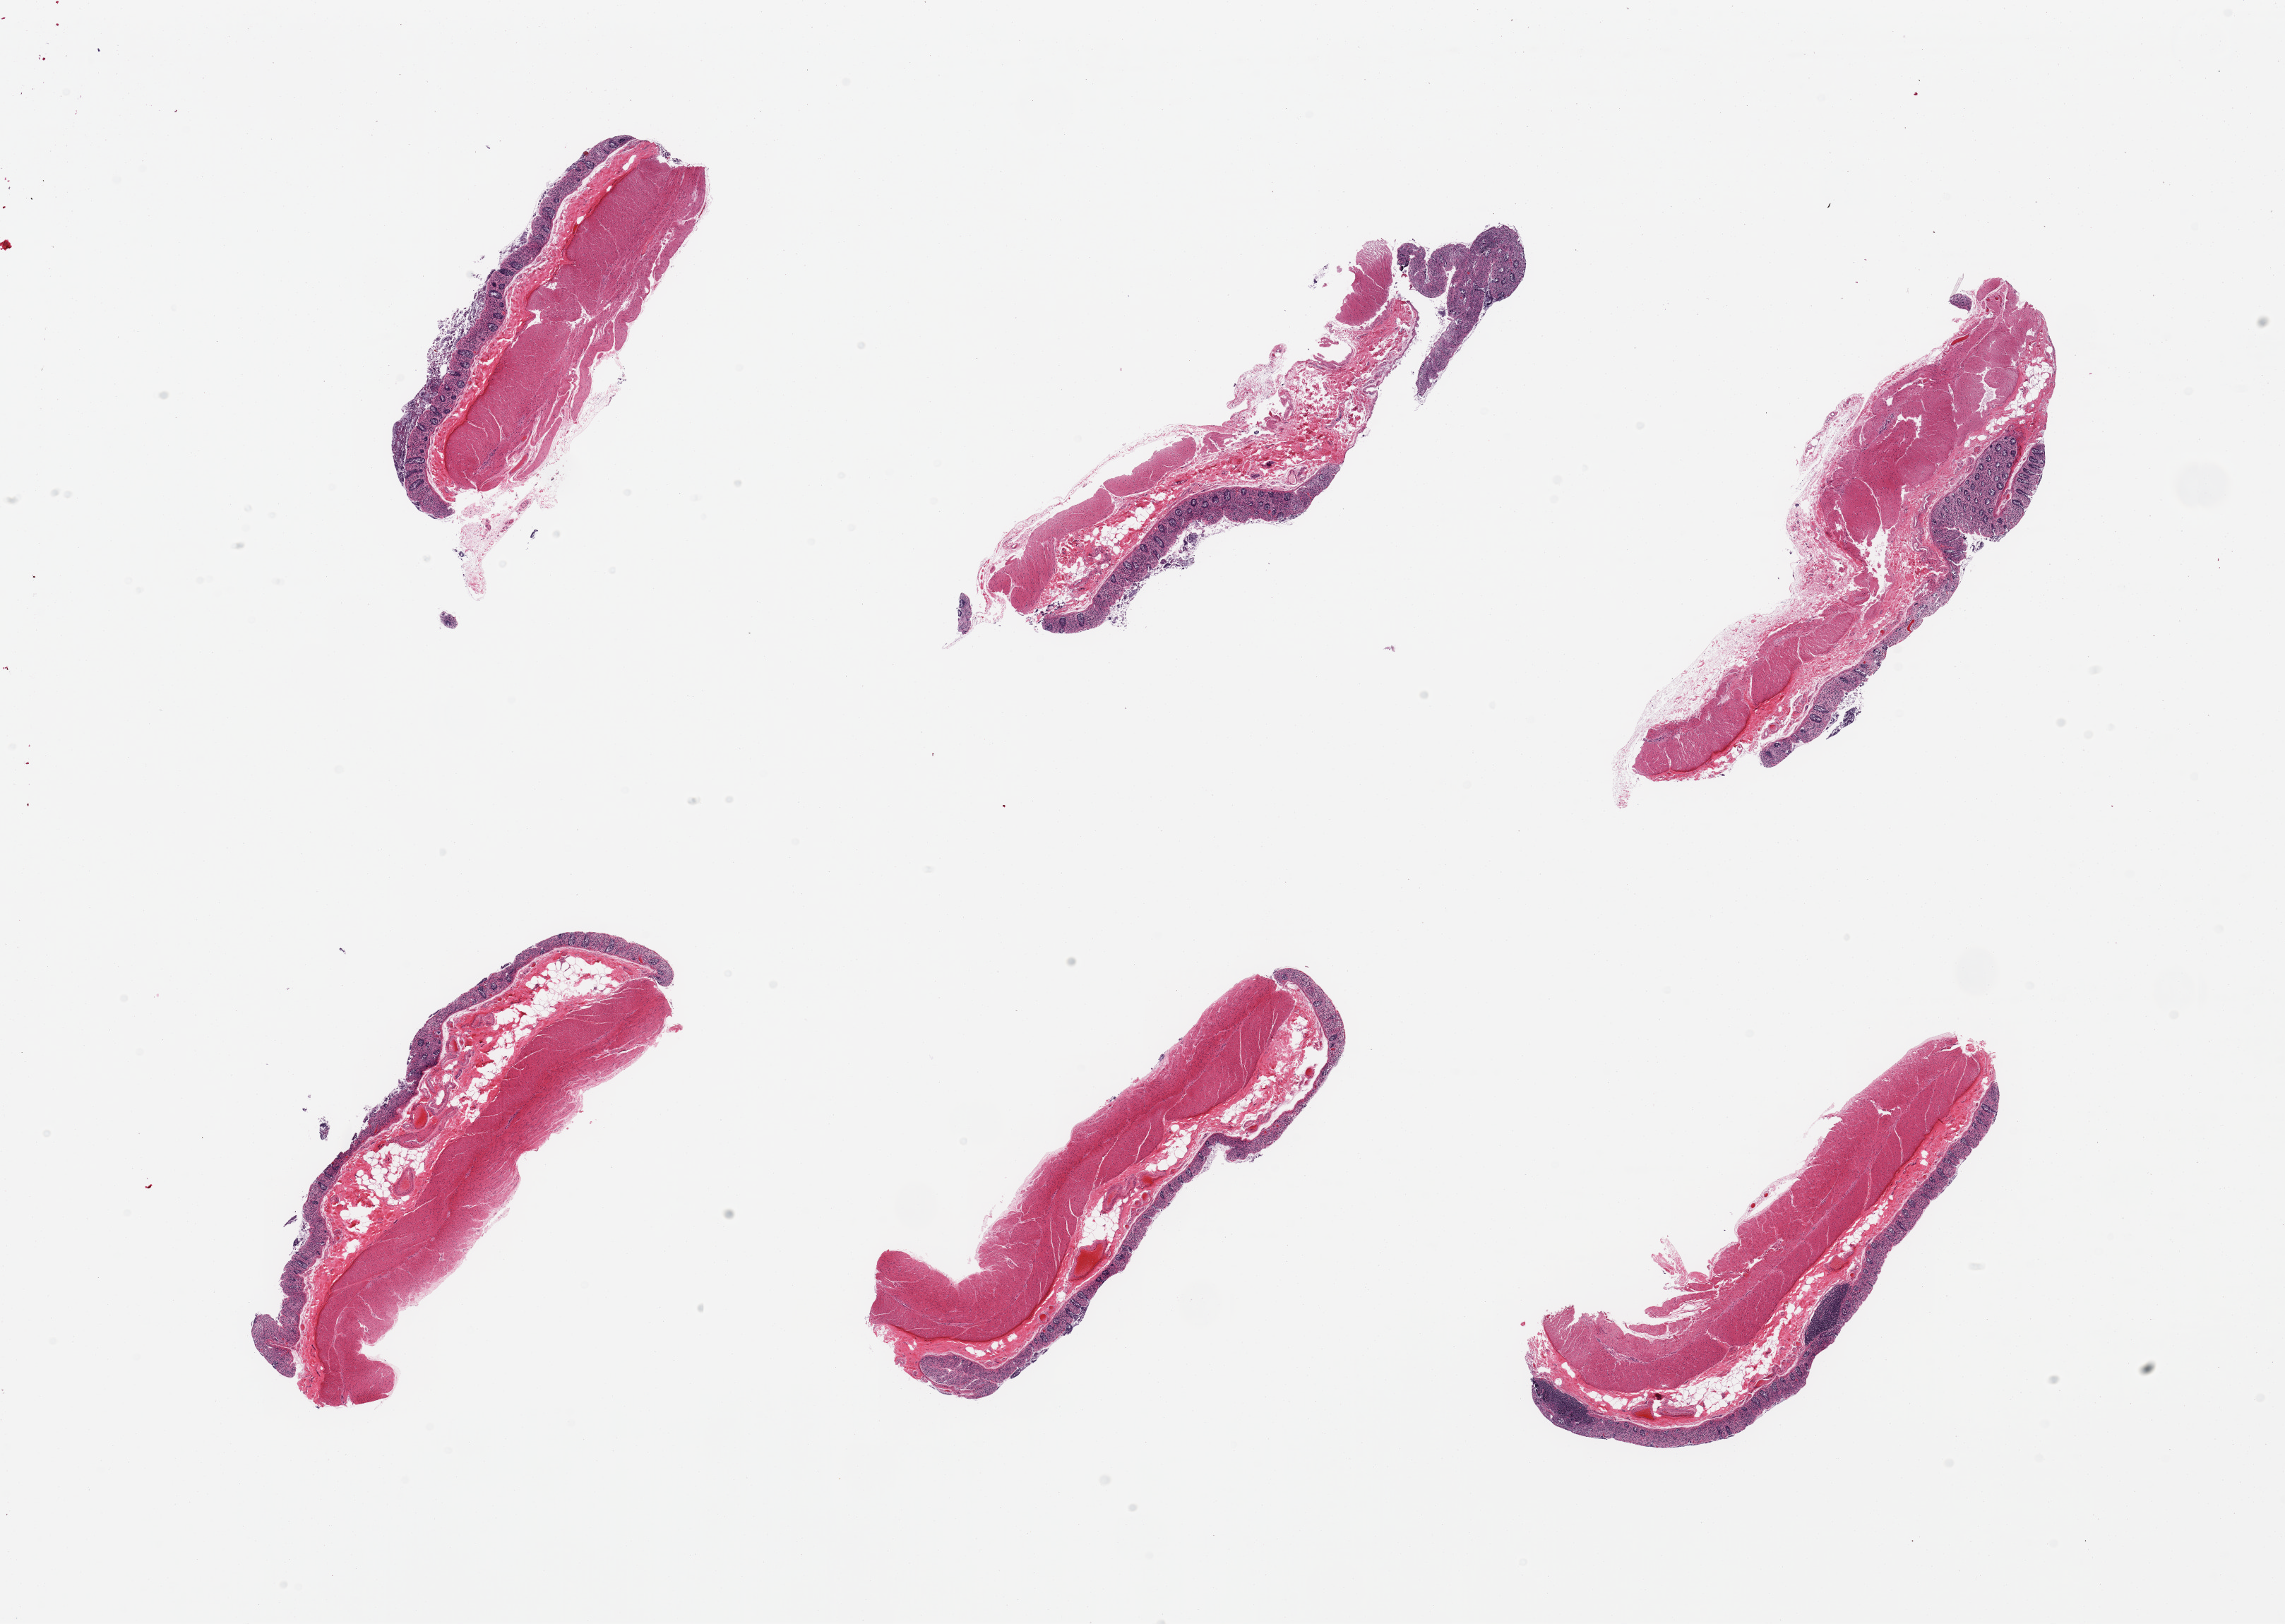
Whole-slide image, hematoxylin and eosin (H&E) stain, brightfield, whole scanned area (about 25.6 x 18.2 mm) shown as a low-resolution overview. PAXgene-fixed paraffin-embedded (PFPE) section. Section of transverse colon (target tissue). Donor tissue sample. Male donor.
Reviewer comment on this tissue sample: 6 pieces; mucosa severely autolyzed, muscularis intact.